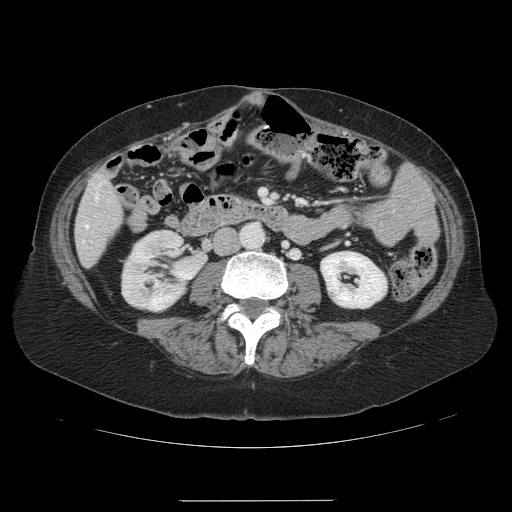
Contrast-enhanced abdominal CT, one axial slice. Position 25 of 141 along the scan axis. 120 kVp. Intravenous contrast given. Soft-tissue window (W 400 / L 40 HU). 2.5 mm slice thickness. 512 × 512 image matrix. Female patient, age 74 years. Case-level facts recorded for this patient, not image findings: diagnosis: colorectal cancer liver metastases, imaged before liver resection; multiple liver metastases: yes; largest metastasis: 7 cm; chemotherapy before resection: no.
Outlined on this slice (outlined manually by an expert reader):
- hepatic veins: bounding box <86,195,97,227> (left, top, right, bottom; pixels)
- liver: <76,175,122,266>
- planned liver remnant (the part of the liver to remain after resection): <84,175,105,266>